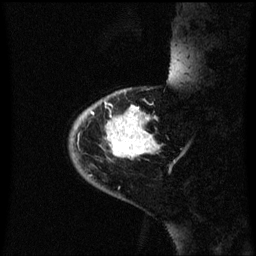
Breast MRI (dynamic contrast-enhanced), one sagittal slice. Slice 12 of 60 in the series (ordered by position). Dynamic contrast-enhanced series, image 2 of 3 at this slice position (ordered by acquisition). 1.5 T. TE 4.2 ms, TR 8.4 ms. 2.3 mm slice thickness. 256 × 256 image matrix. Patient: female, 46 years. Case-level facts recorded for this patient, not image findings: setting: breast cancer imaged before/during neoadjuvant chemotherapy; receptor status: HER2-positive.
Annotated regions visible in this slice (semi-automatic segmentation, software-assisted and operator-edited):
- analysis volume of interest (the breast-tissue region the enhancement analysis was run in; not a lesion): box from (x=70, y=88) to (x=157, y=171) px
- tumour enhancement mask (voxels above the 70 % enhancement threshold inside the analysis volume of interest): (x=82, y=106)–(x=157, y=157)